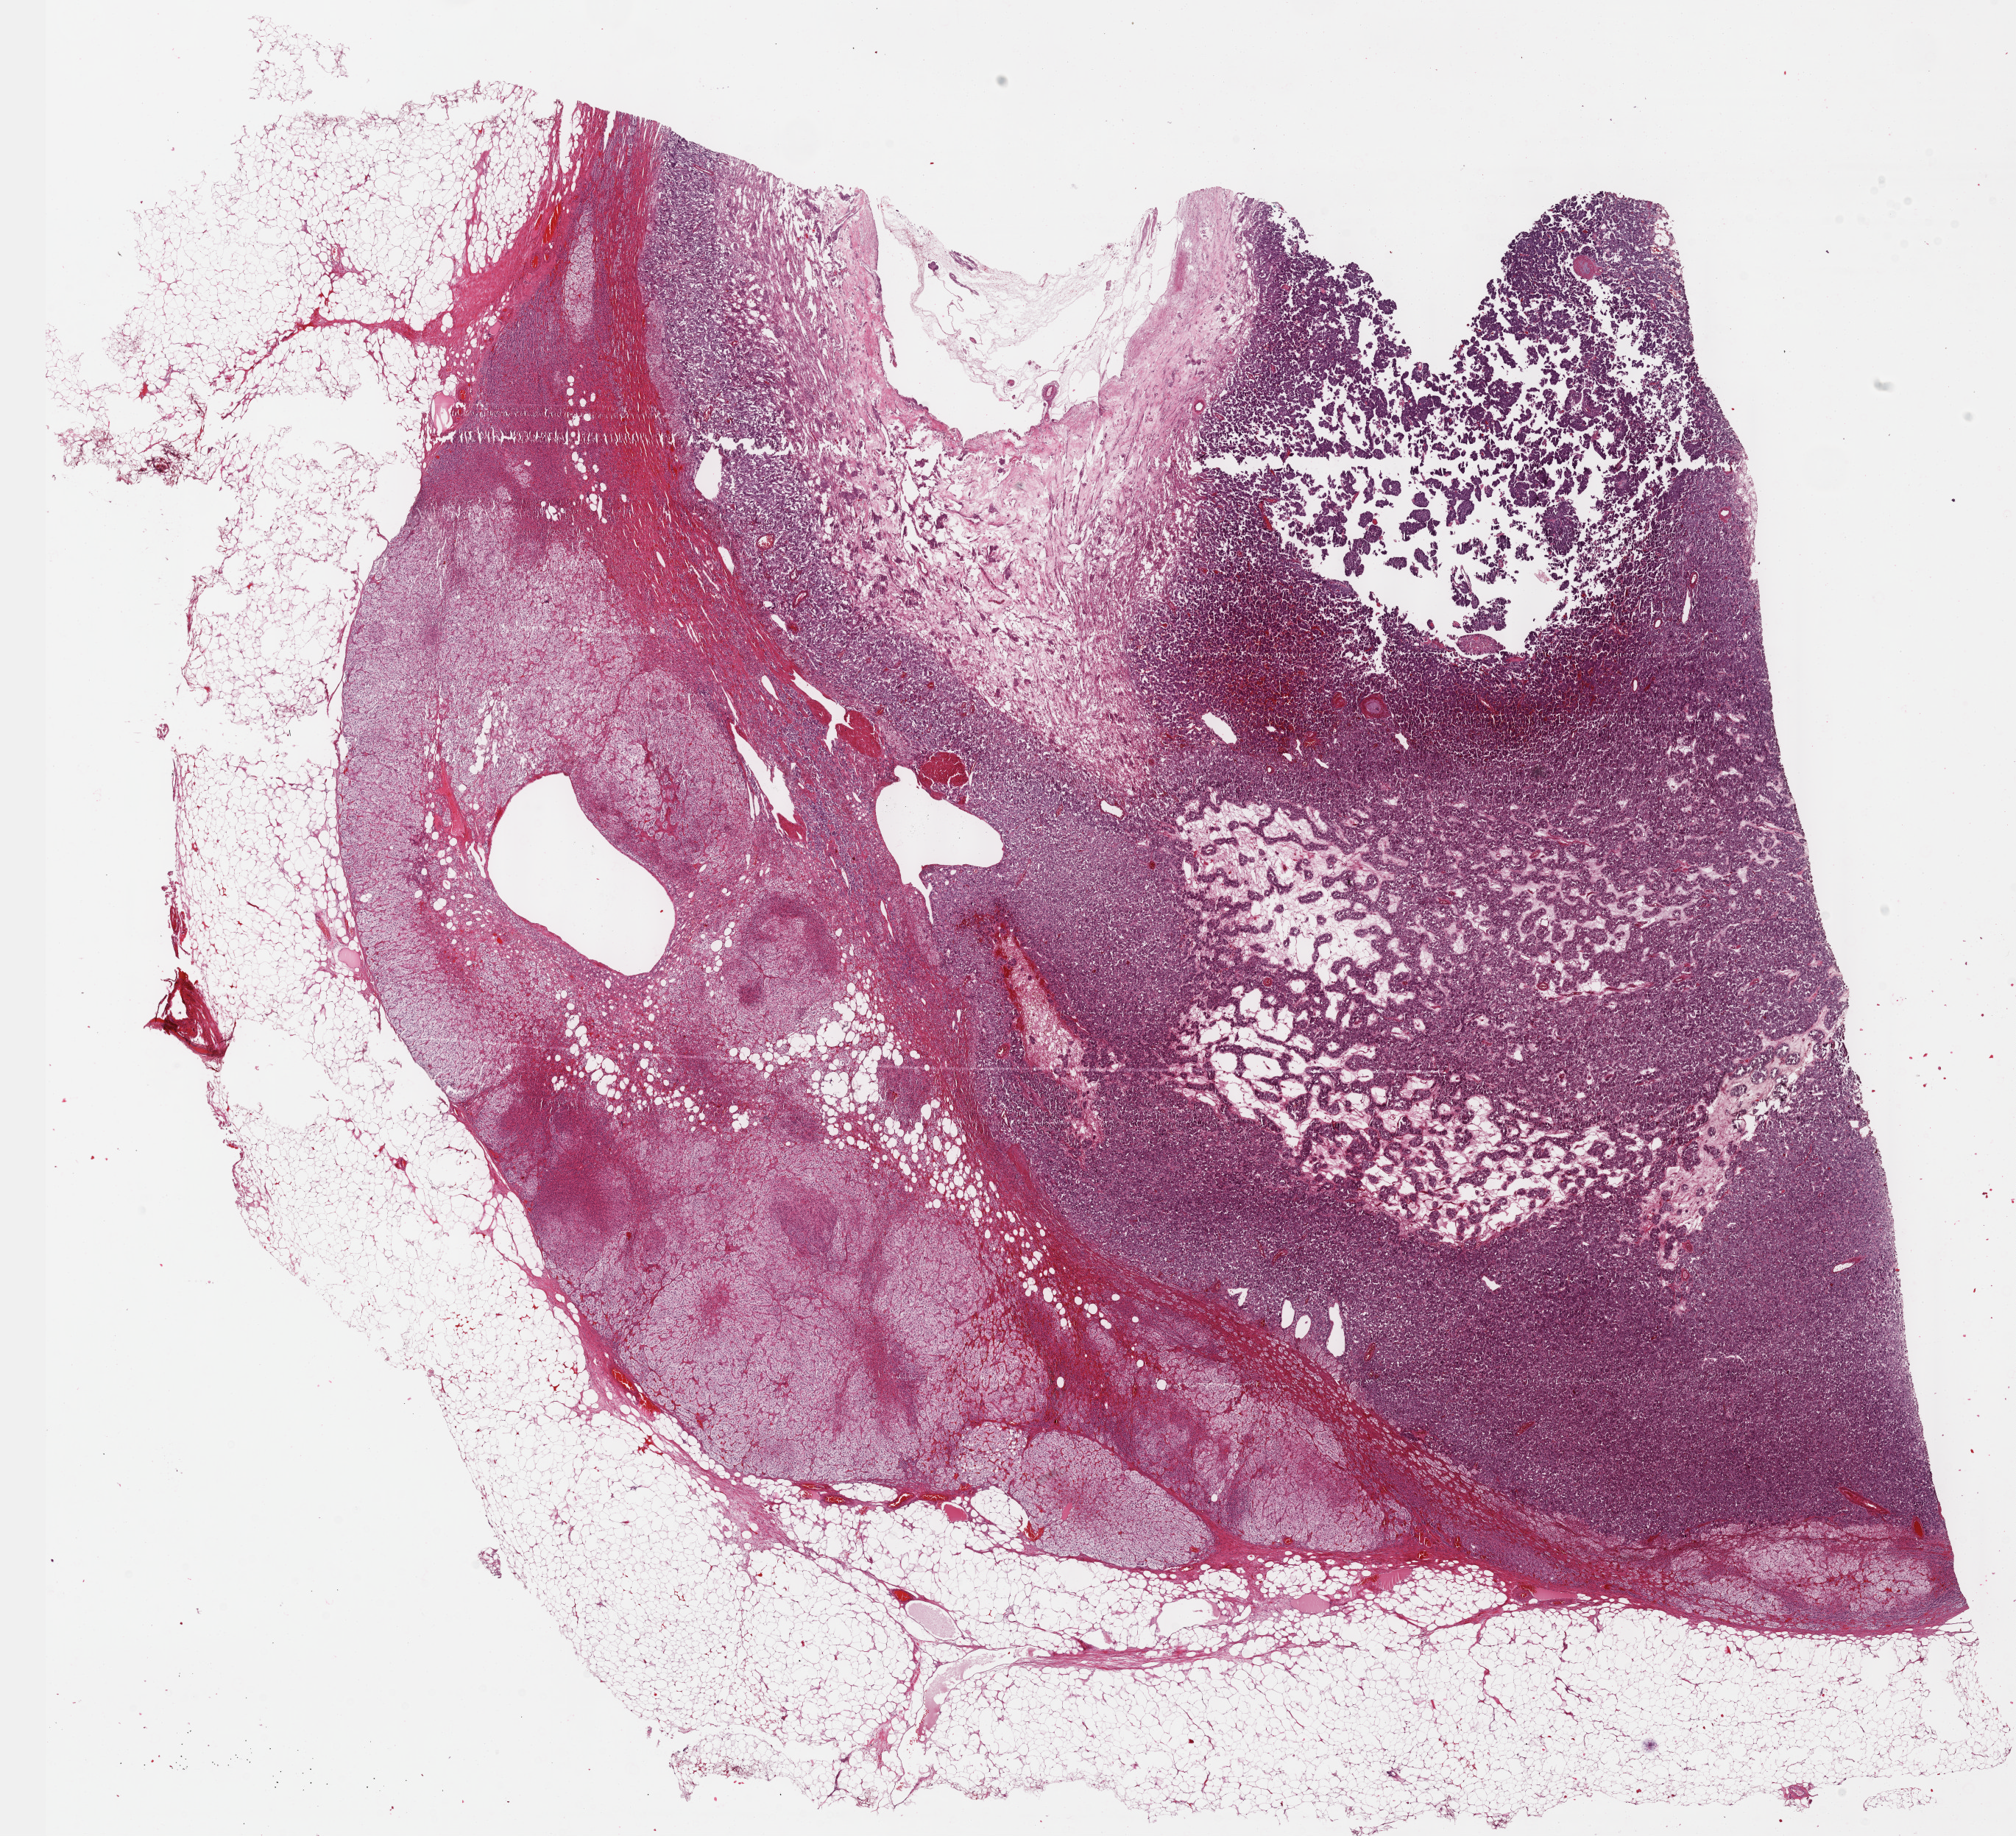
Digitized H&E-stained tissue section (whole slide), a low-resolution overview of the entire scanned area, about 22.1 x 20.2 mm (from a 40x scan); formalin-fixed paraffin-embedded (FFPE) diagnostic section; adrenal gland, primary tumour sample. Patient: male, age at initial diagnosis 54 years.
Histologic diagnosis: Pheochromocytoma, NOS.